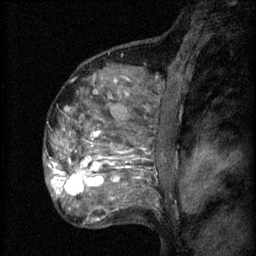
Breast MRI (dynamic contrast-enhanced), one sagittal slice; 3 images stored at this slice position (order not interpretable as contrast timing); 1.5 T; TE 4.2 ms, TR 8.2 ms; 2 mm slice thickness; 256 × 256 image matrix, field of view 180 × 180 mm. Patient: female, 48 years.
Annotated regions visible in this slice (semi-automatic segmentation, software-assisted and operator-edited):
- analysis volume of interest (the breast-tissue region the enhancement analysis was run in; not a lesion): box from (x=61, y=138) to (x=153, y=201) px
- tumour enhancement mask (voxels above the 70 % enhancement threshold inside the analysis volume of interest): (x=61, y=158)–(x=120, y=199)